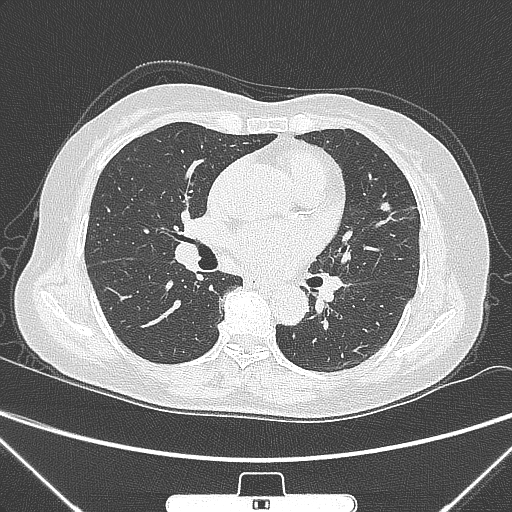
Chest CT, one axial slice. Position 145 of 300 along the scan axis. 120 kVp. Lung window (W 1500 / L -600 HU). 1 mm slice thickness. 512 × 512 image matrix. Female patient, age 70 years. From the clinical record (not read from this slice): clinical TNM (as recorded): T1b N0 M0.
Structures marked on this image (bounding box drawn by a radiologist):
- lung tumour (recorded histology: adenocarcinoma): bounding box (x1, y1, x2, y2) in pixels: (372, 195, 394, 219)